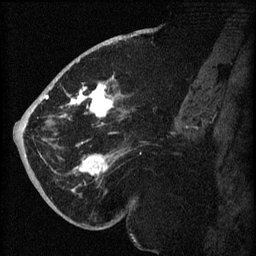
Breast MRI (dynamic contrast-enhanced), one sagittal slice; position 34 of 60 along the scan axis; dynamic contrast-enhanced series, image 2 of 3 at this slice position (ordered by acquisition); 1.5 T; TE 4.2 ms, TR 8.2 ms; 256 × 256 image matrix. Female patient, age 71 years.
Annotated regions visible in this slice (semi-automatic segmentation, software-assisted and operator-edited):
- analysis volume of interest (the breast-tissue region the enhancement analysis was run in; not a lesion): bounding box (x1, y1, x2, y2) in pixels: (40, 72, 135, 196)
- tumour enhancement mask (voxels above the 70 % enhancement threshold inside the analysis volume of interest): (42, 82, 117, 192)